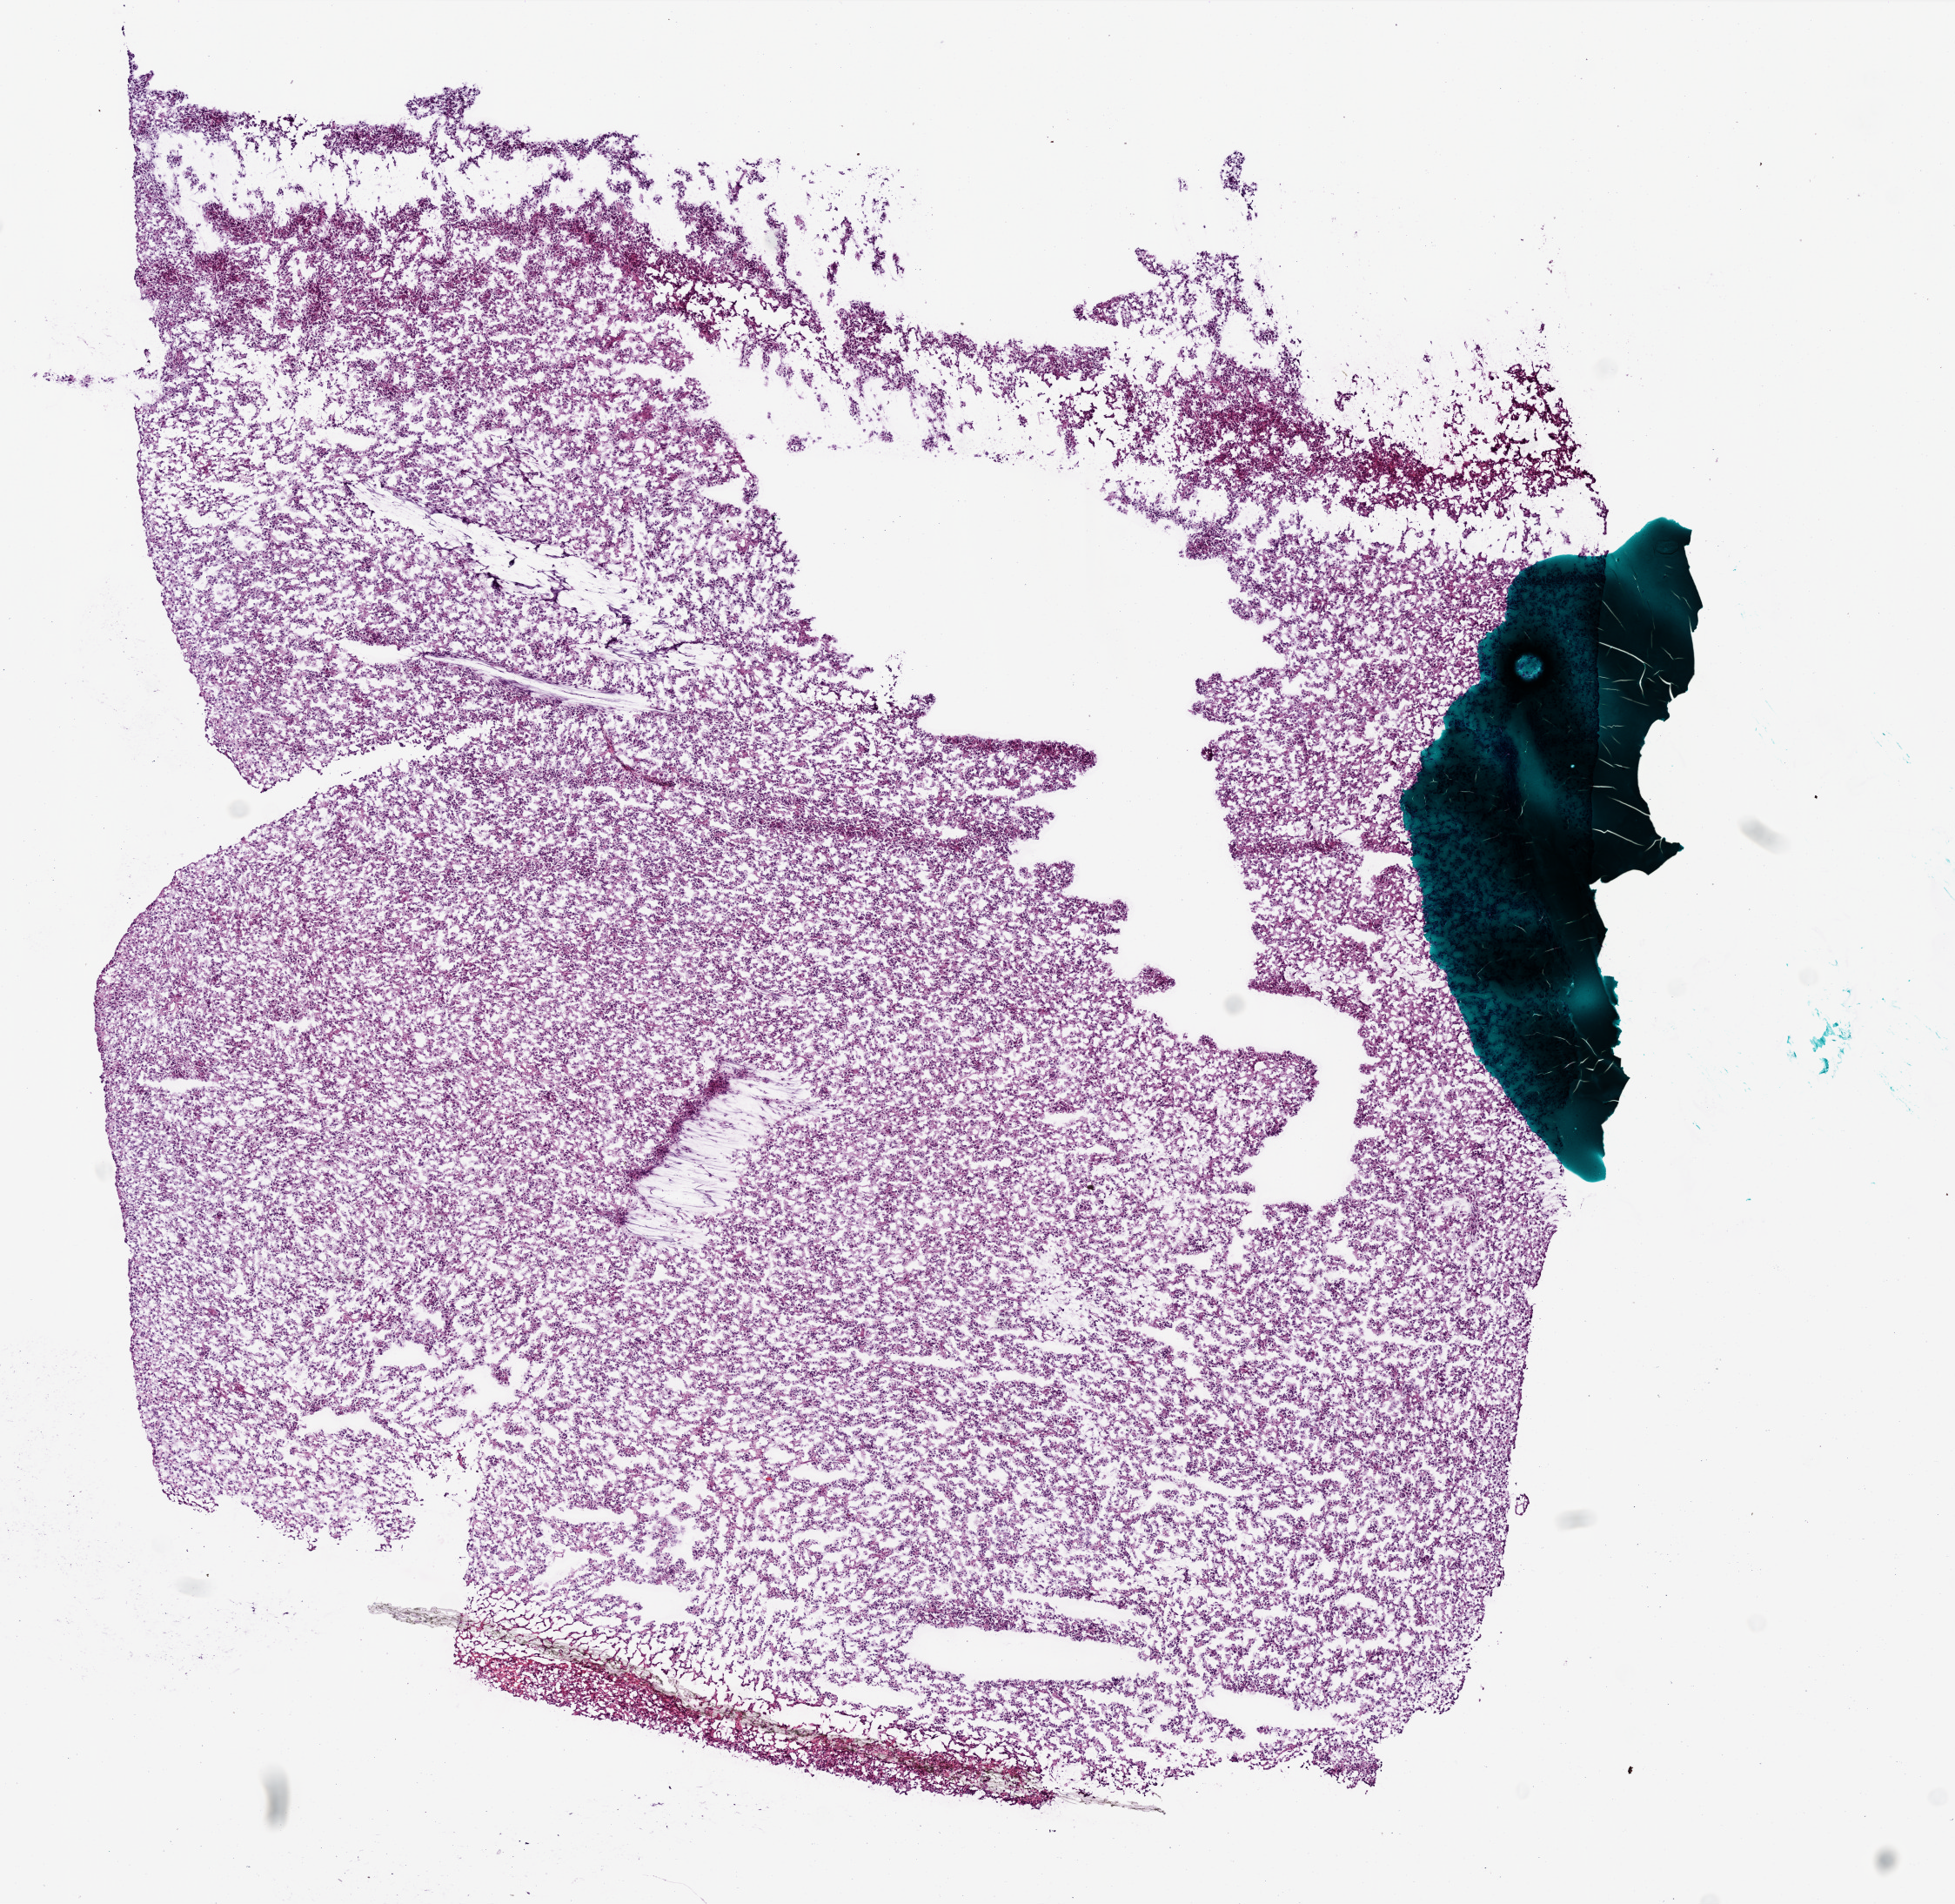
Whole-slide histology image, H&E, whole scanned area (about 9.0 x 8.8 mm, slide scanned at 20x) shown as a low-resolution overview, frozen section from the bottom of the tissue portion, brain, primary tumour sample. Patient: female, age at initial diagnosis 36 years. Slide review estimates, as recorded: tumour cells 100%, tumour nuclei 95%, stromal cells 0%, necrosis 0%.
* histologic diagnosis: Glioblastoma